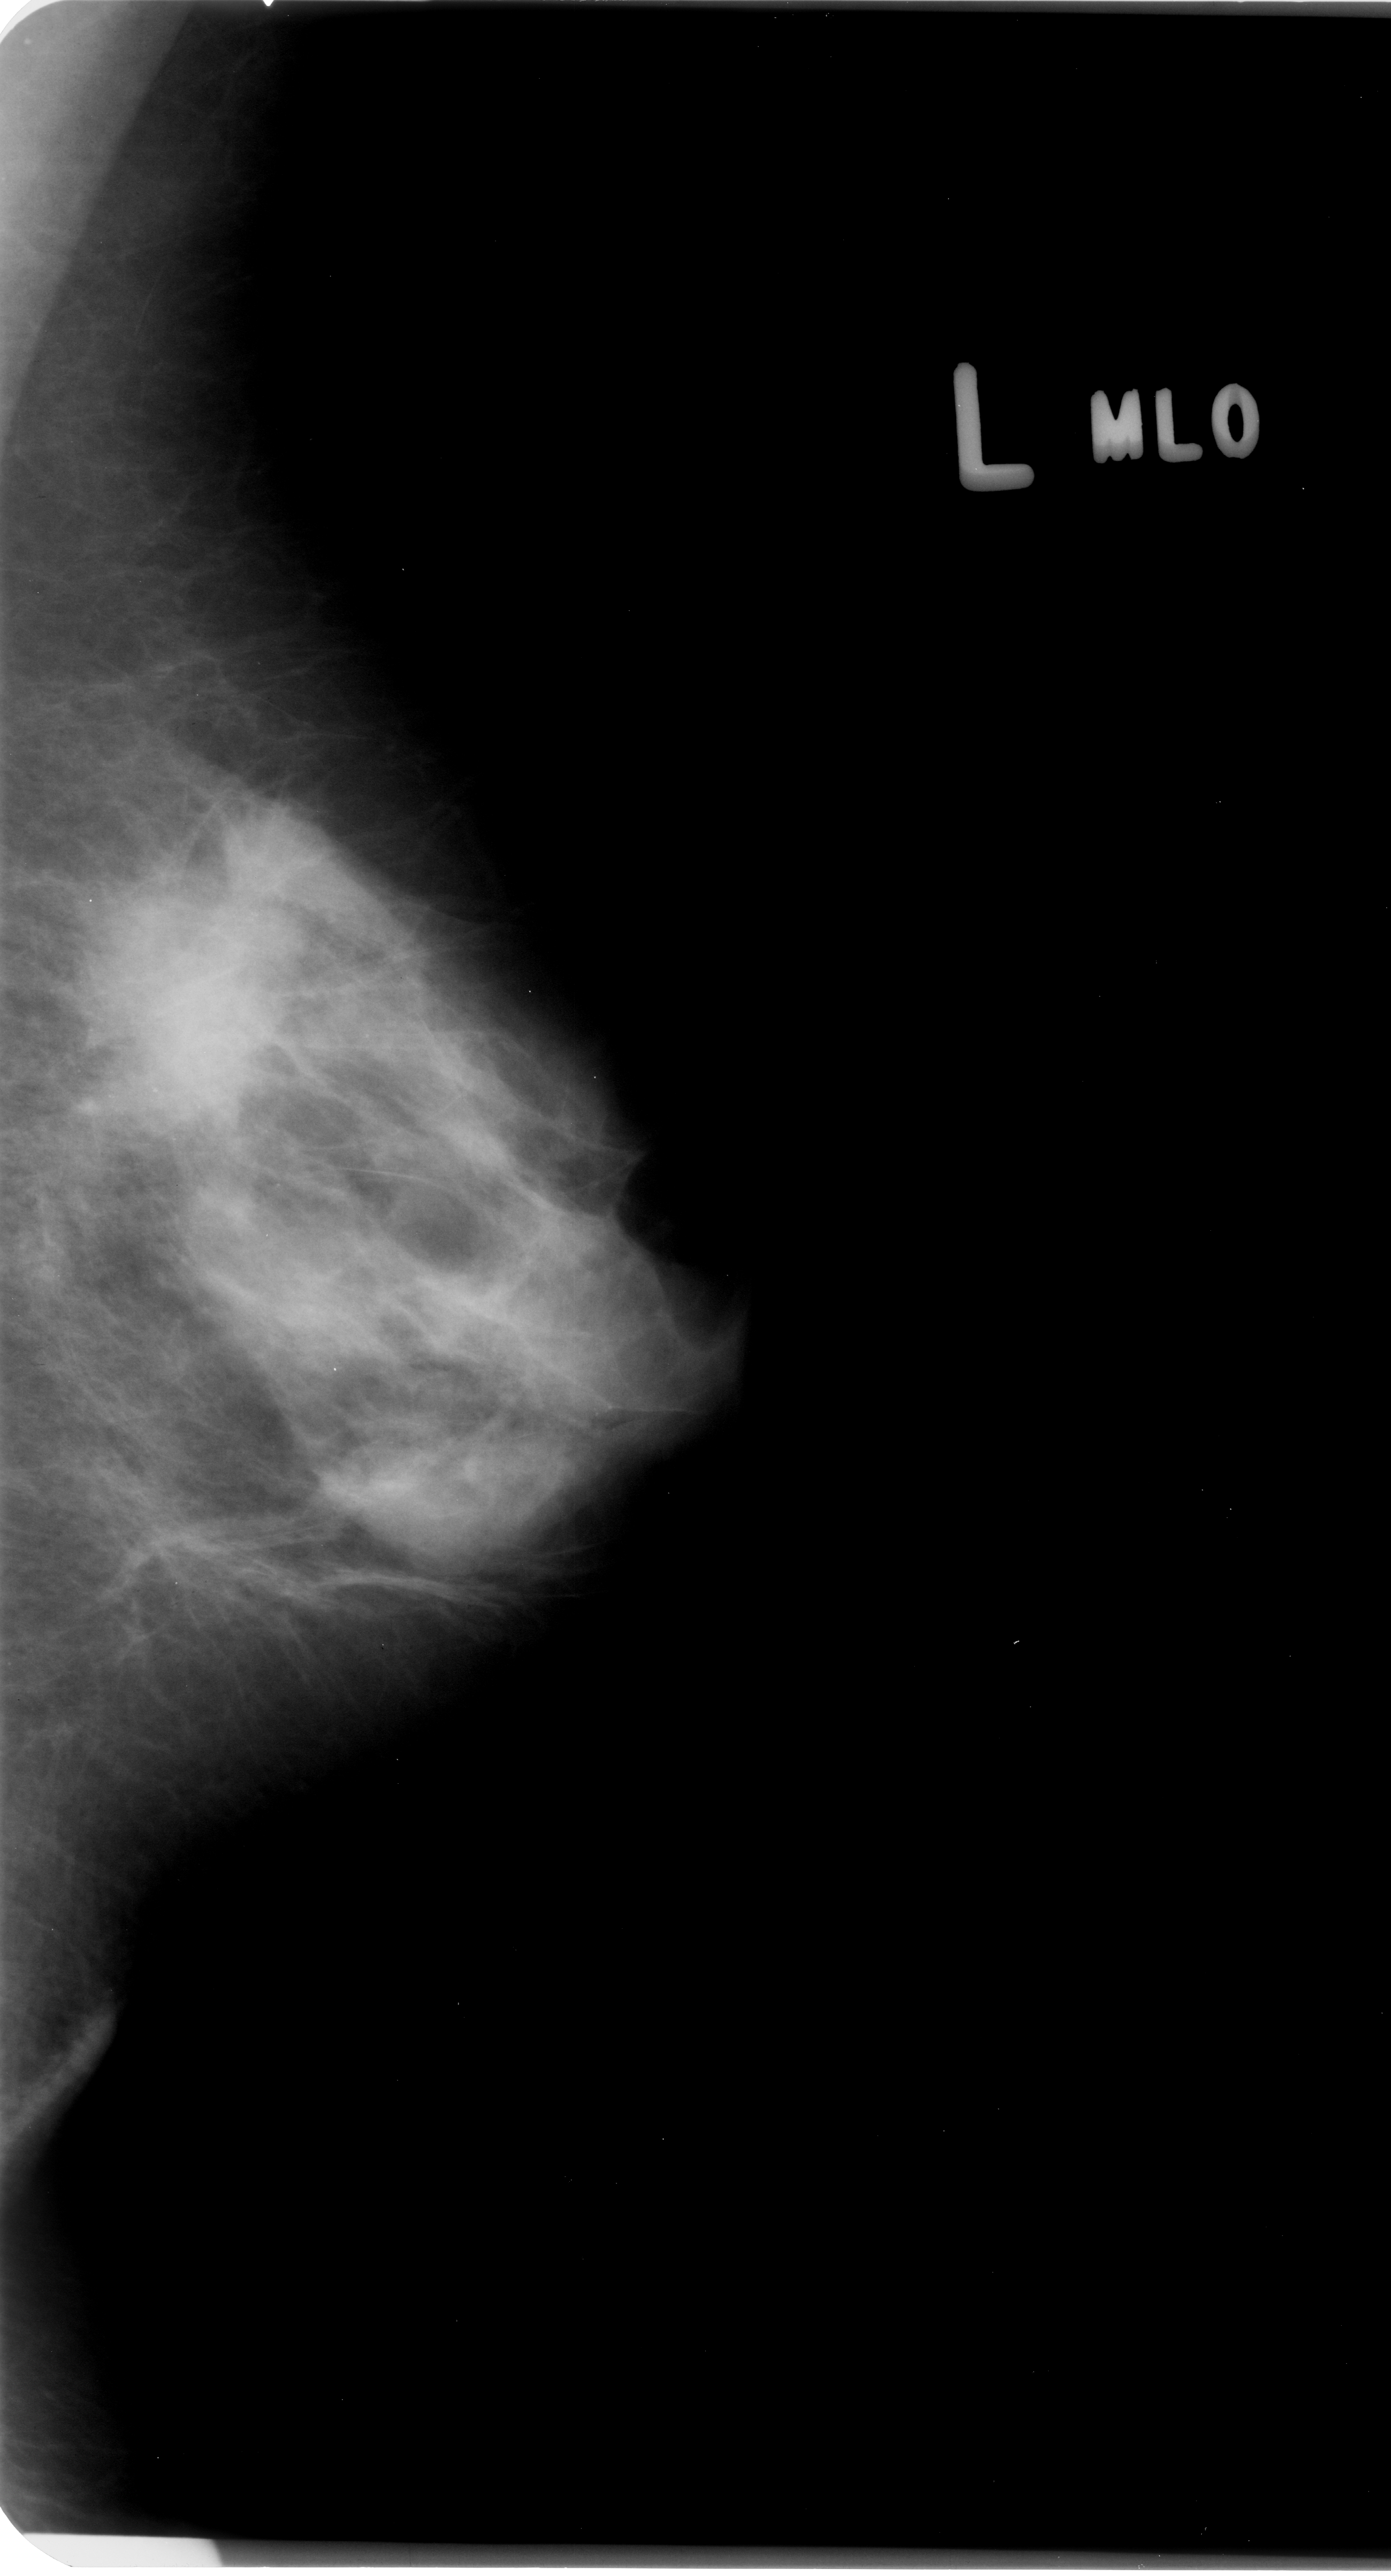
Scanned film-screen mammogram, left breast, mediolateral oblique (MLO) view, BI-RADS breast density category 3 (scale 1–4).
Radiologist-marked abnormalities on this image: Finding 1 of 2: calcifications, morphology amorphous / round and regular, distribution clustered; BI-RADS assessment category 4; pathology (as recorded): malignant. Finding 2 of 2: calcifications, morphology amorphous / round and regular, distribution clustered; BI-RADS assessment category 4; pathology result (as recorded, not read from the image): malignant.